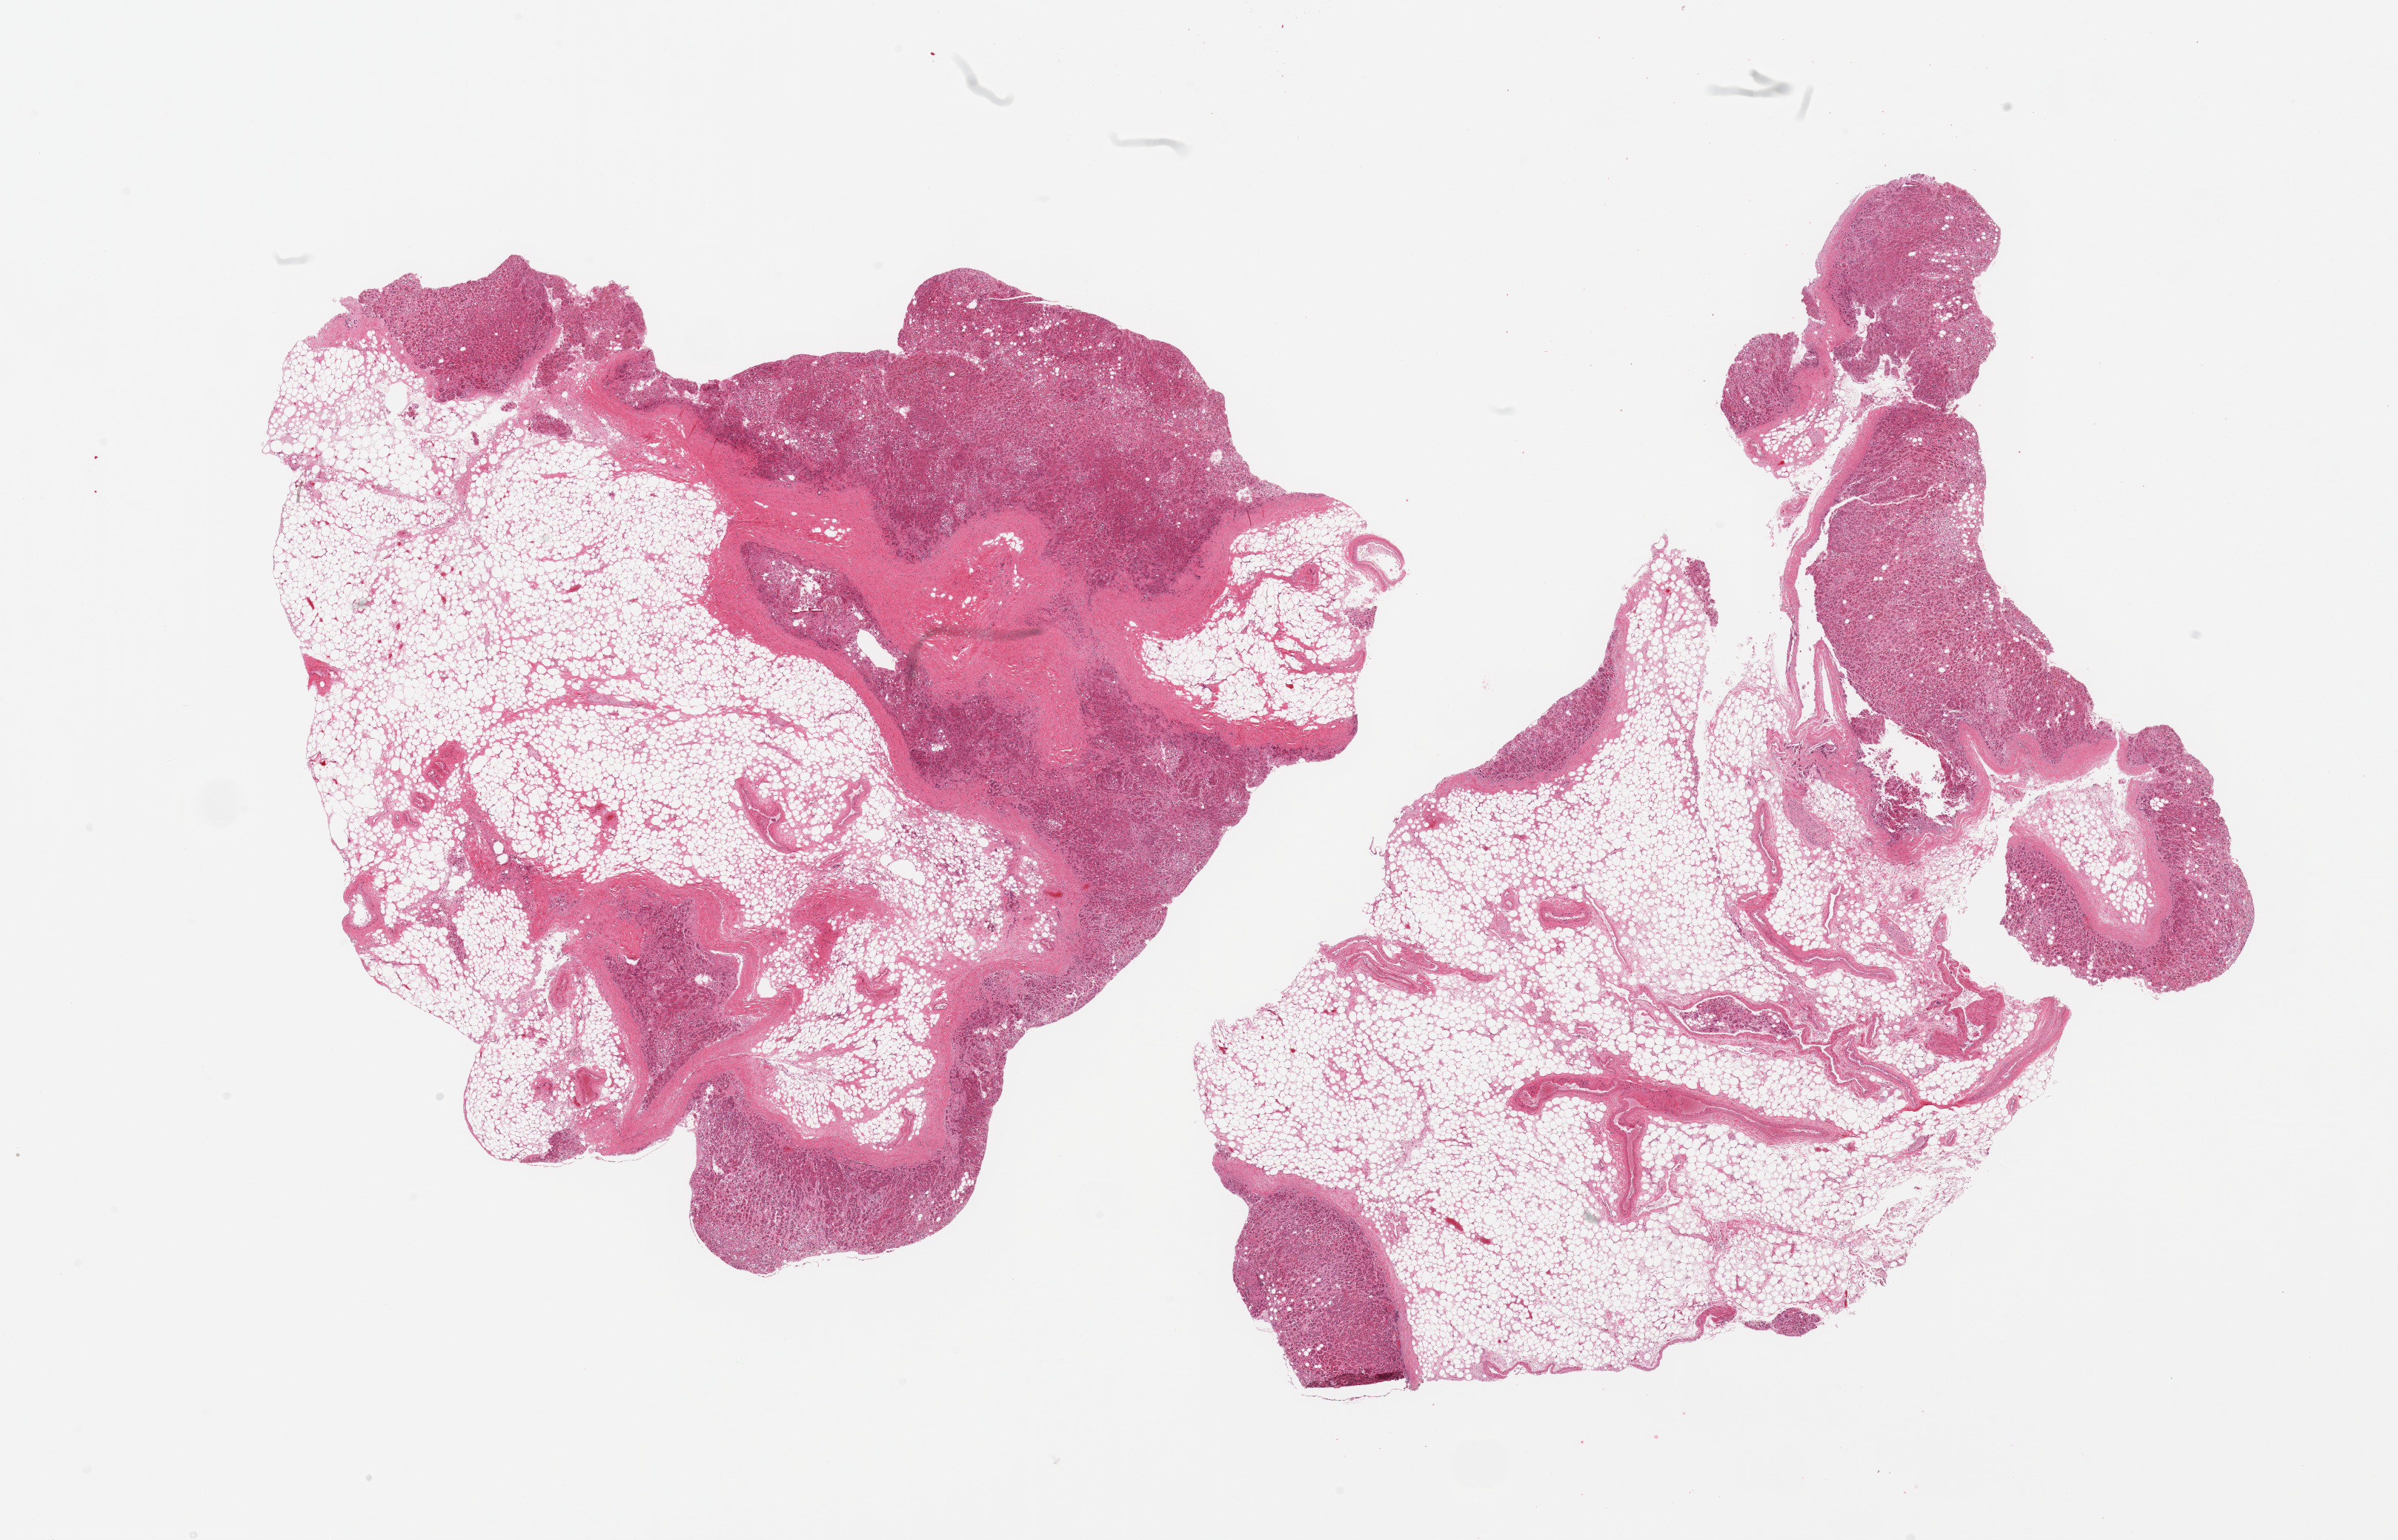
Whole-slide image, H&E stain — shown as a low-resolution overview of the whole scanned area (about 25.6 x 16.4 mm), PAXgene-fixed paraffin-embedded (PFPE) section, target tissue: adrenal gland, tissue donor sample. Donor: male.
- reviewer comment on this tissue sample: 2 pieces, ~60-70% fat, rest is badly autolyzed cortex